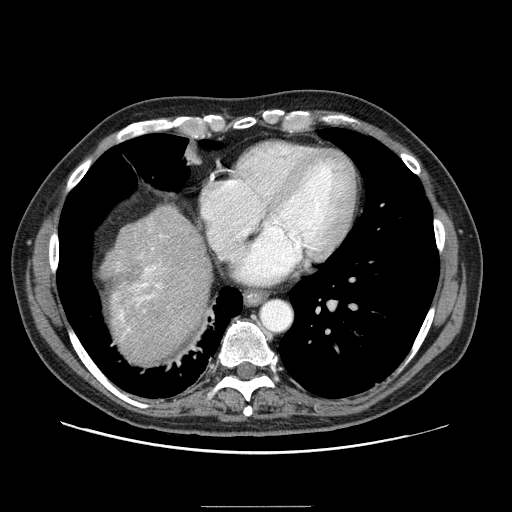
Contrast-enhanced abdominal CT (liver protocol), one axial slice. Slice 83 of 99 in the series (ordered by position). Reconstruction kernel STANDARD. 100 kVp. One of 2 acquisitions stored at this slice position. Soft-tissue window (W 400 / L 40 HU). 512 × 512 image matrix, field of view 400 × 400 mm. Case-level facts recorded for this patient, not image findings: diagnosis: hepatocellular carcinoma (patient treated with transarterial chemoembolisation; whether this scan precedes or follows treatment is not stated here); TNM stage (as recorded): Stage-II; Child-Pugh class: A; tumour nodularity: multinodular; tumour size: 3.2 cm.
Outlined on this slice (semi-automatically segmented with operator editing):
- liver parenchyma outside the tumour (the mass and vessels are separate outlines, so this box may not span the whole liver): bounding box <103,204,210,362> (left, top, right, bottom; pixels)
- liver vessels: <114,235,163,335>